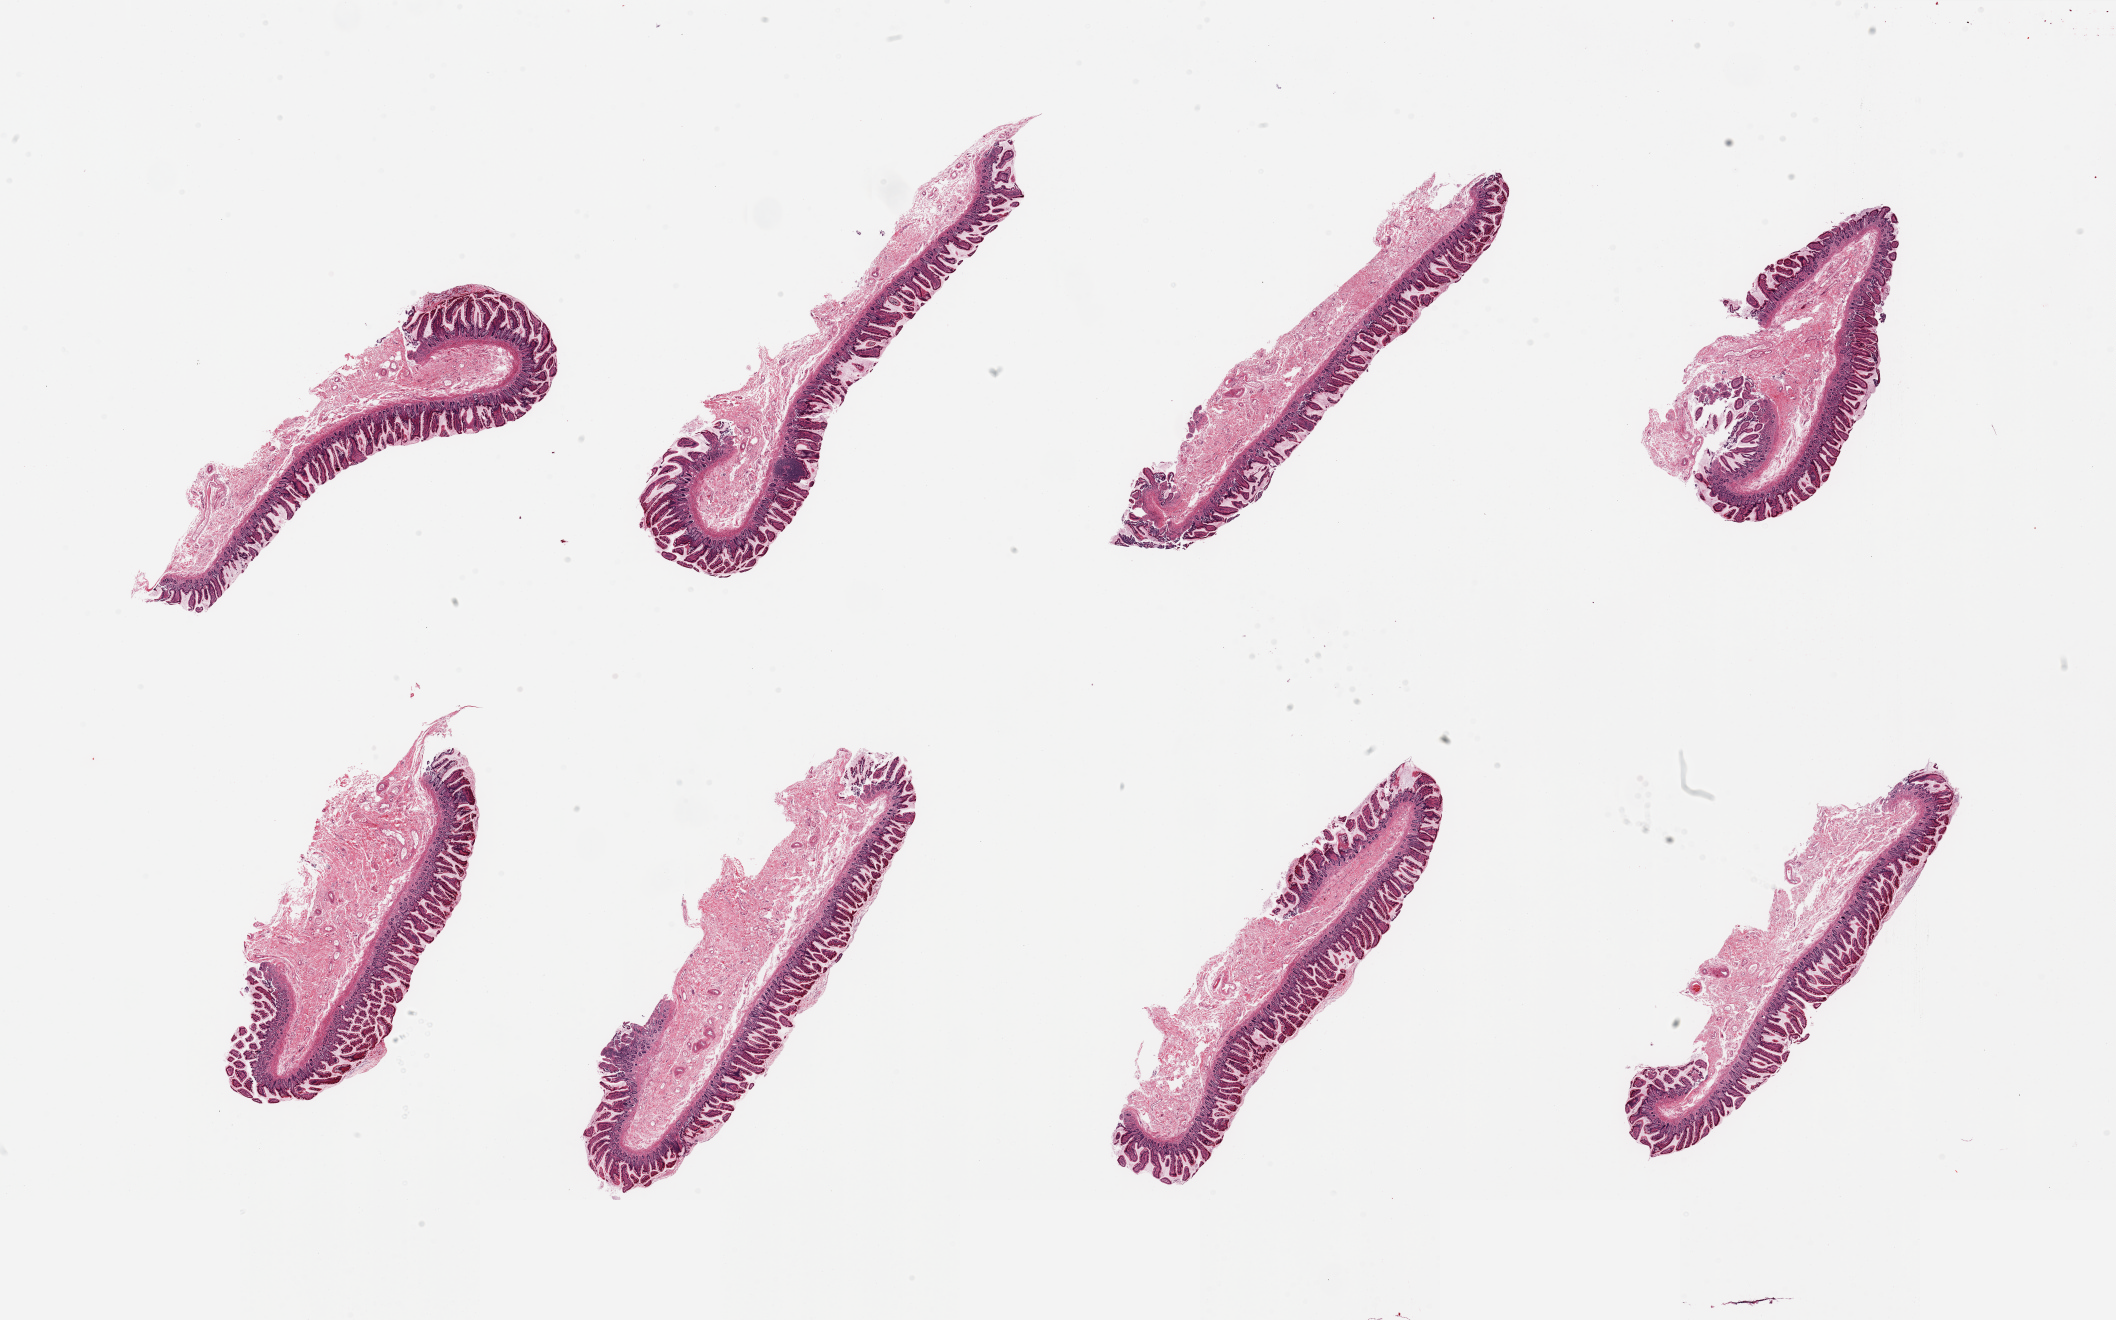
Digitized H&E-stained section, brightfield — shown as a low-resolution overview of the whole scanned area (about 33.5 x 20.9 mm), PAXgene-fixed paraffin-embedded (PFPE) section, target tissue: ileum, tissue donor sample. Male donor.
Reviewer comment on this tissue sample: 8 pieces; well preserved, but with minimal lymphoid tissue.